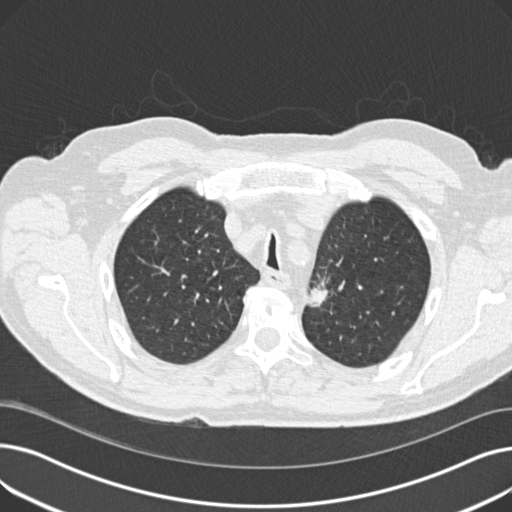
Chest CT (low-dose screening protocol), one axial image; third screening round (two years after baseline); lung window (W 1500 / L -600 HU); standard (soft-tissue) reconstruction kernel (B30f); slice 46 of 191 in the series; 512 × 512 image matrix. Male participant, aged 70 years at enrolment.
Lesion marked by an expert reader, bounding box (x1, y1, x2, y2) in pixels: (301, 269, 341, 312). The screening reader recorded 2 non-calcified nodules or masses ≥4 mm on this exam (left upper lobe, left lower lobe); which of them this box marks is not recorded. Official screen result: positive, other. Participant outcome: lung cancer diagnosed 175 days after this screen — mixed cell adenocarcinoma, left upper lobe, poorly differentiated (G3), stage IIB (AJCC 6th edition), 17 mm at pathology.